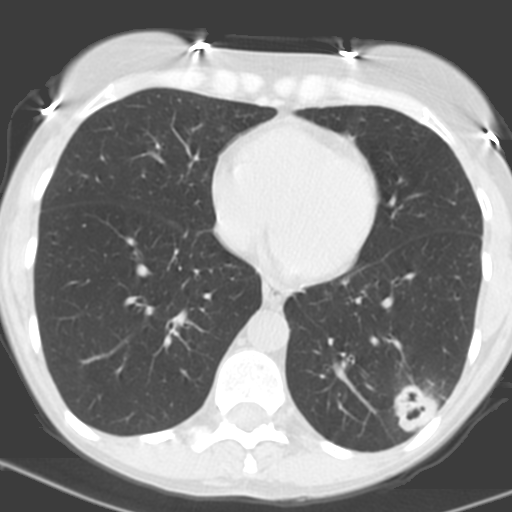
Low-dose screening chest CT, one axial slice; slice 59 of 156 in the series (ordered by position); 120 kVp; lung window (W 1500 / L -600 HU); 3.2 mm slice thickness; 512 × 512 image matrix, field of view 262 × 262 mm.
Annotated regions visible in this slice (expert manual segmentation):
- lesion 1 (tumor, lower lobe of left lung): bounding box [x1, y1, x2, y2] px = [394, 384, 438, 435]